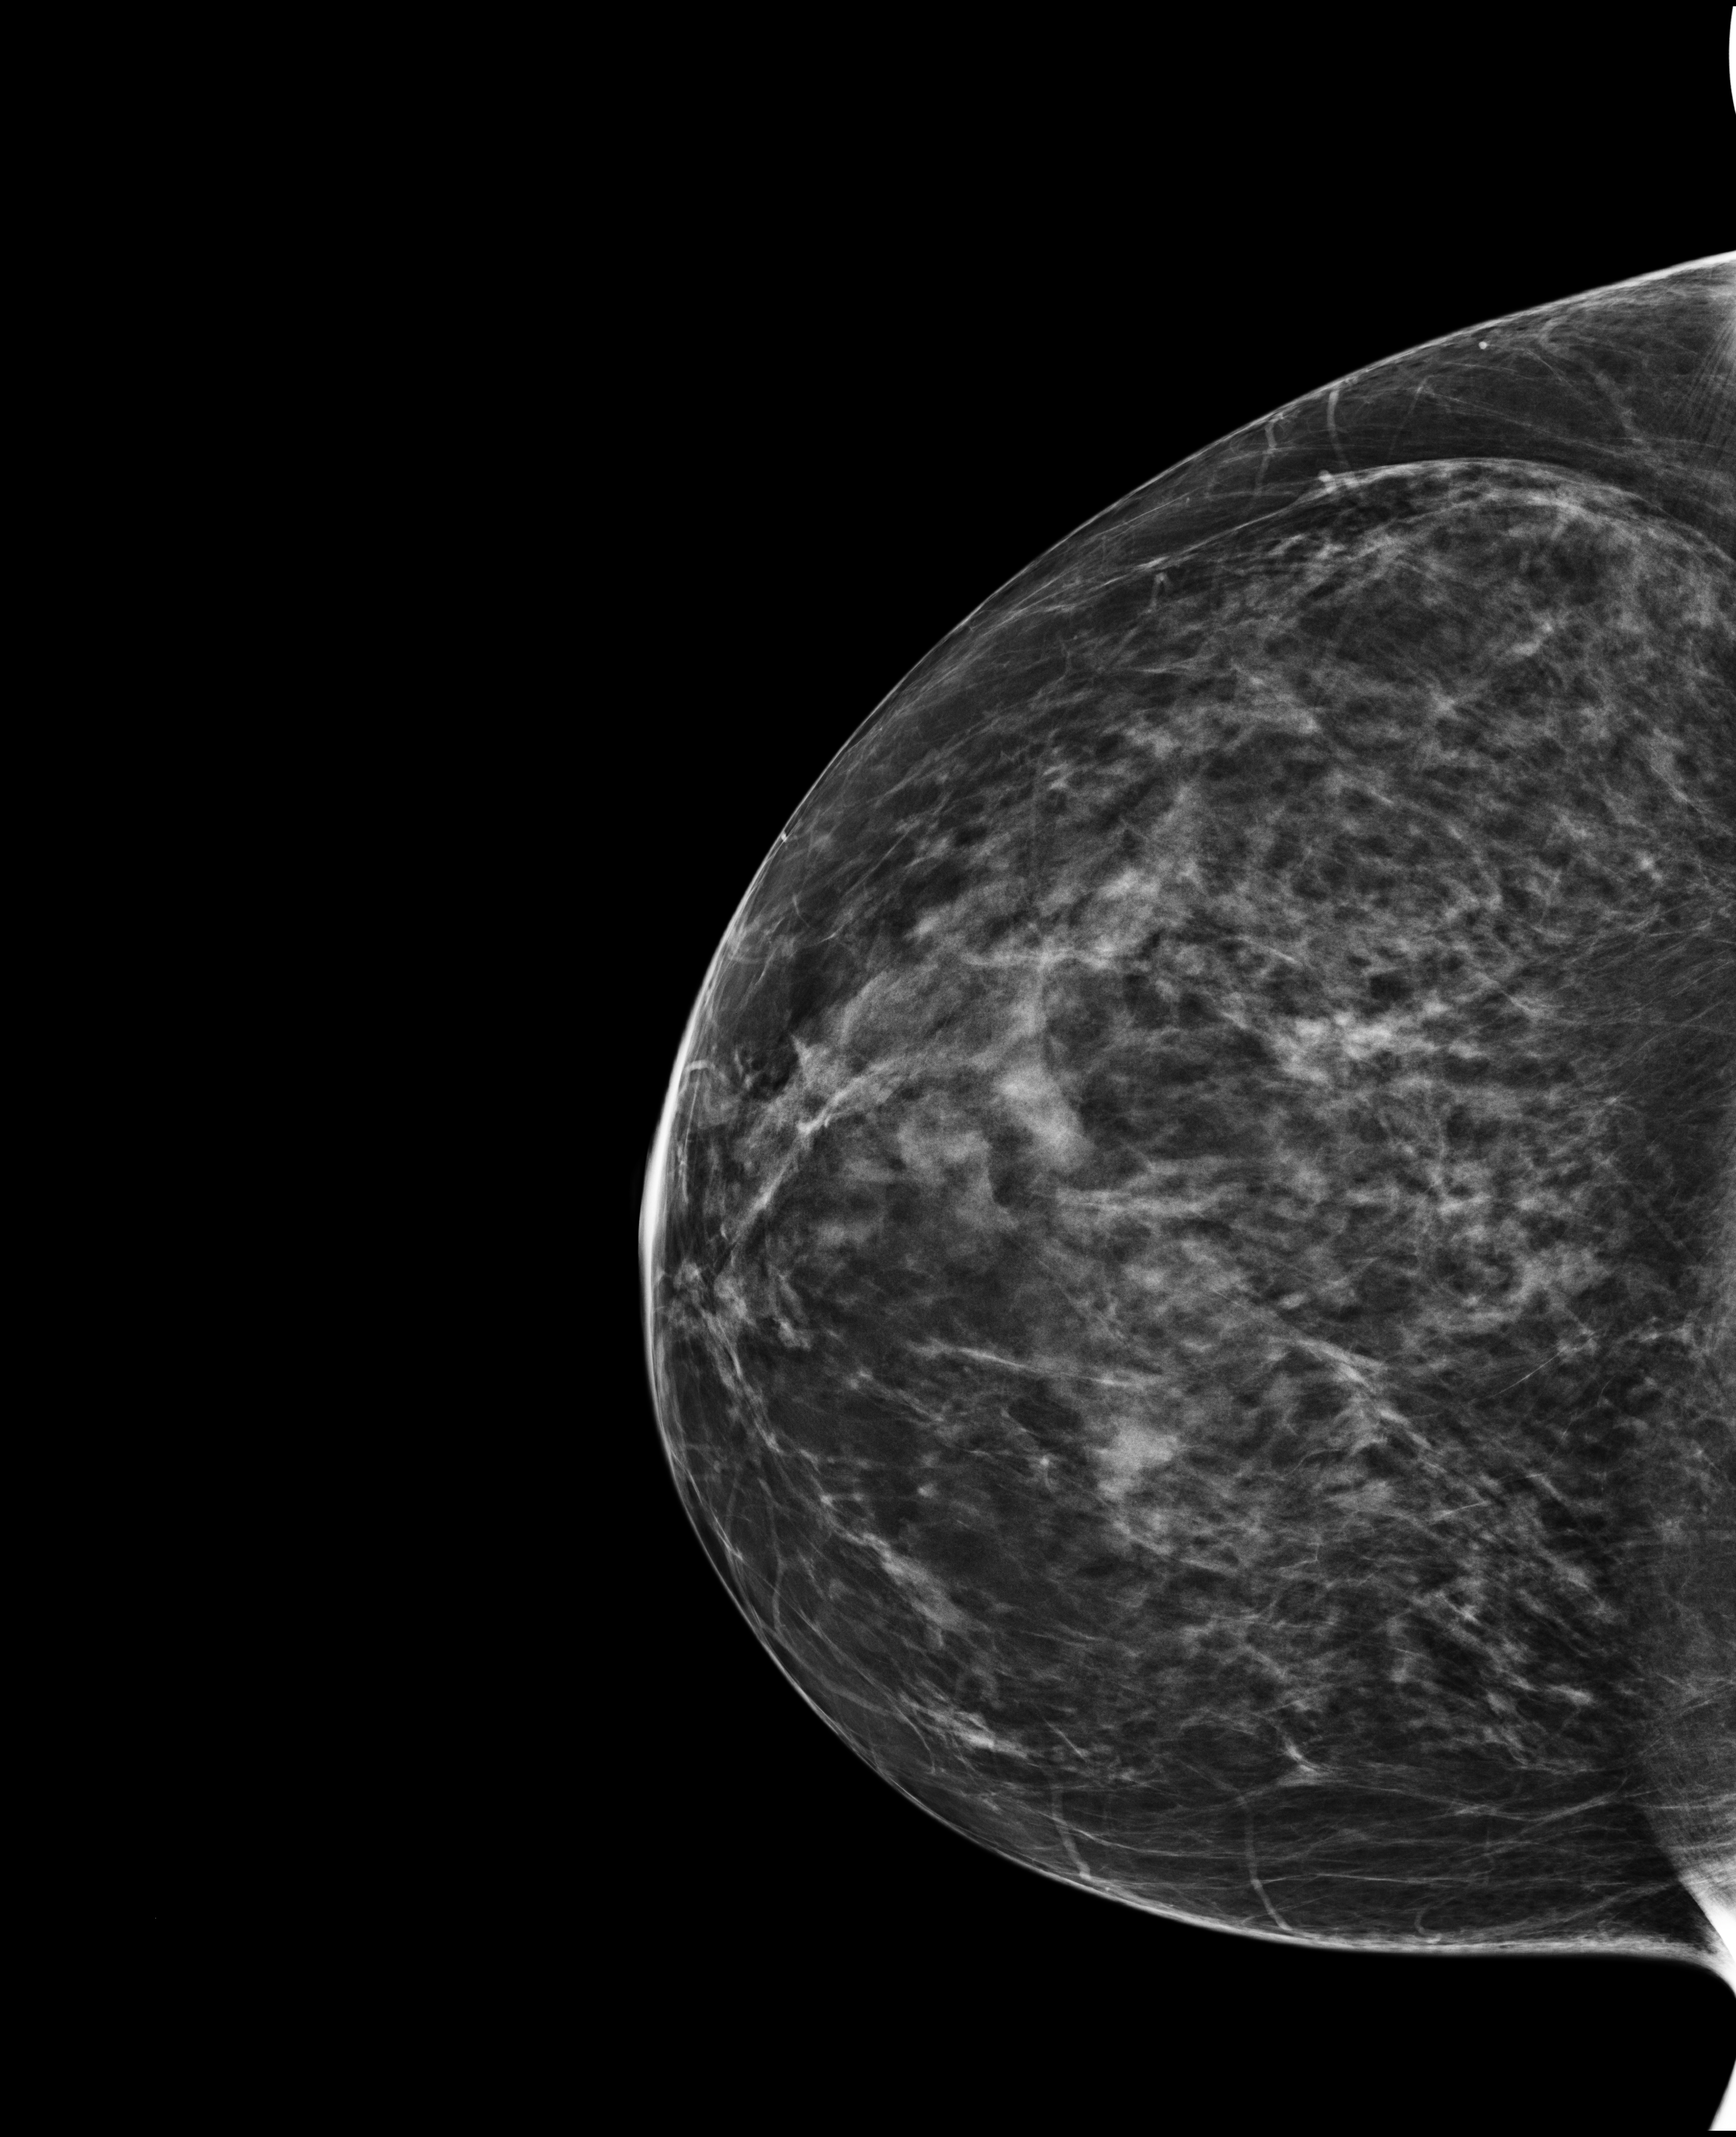
Annual screening mammography examination; compressed breast thickness 67 mm; system: Selenia Dimensions.
Image type: full-field digital mammogram. Breast: right. Projection: cranio-caudal projection.